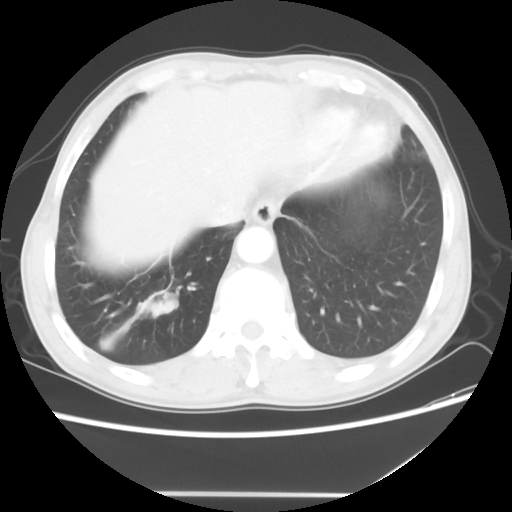
Chest CT, one axial slice; slice 9 of 56 in the series (ordered by position); lung window (W 1500 / L -600 HU); 512 × 512 image matrix, field of view 344 × 344 mm. Patient: male, 65 years. Case-level facts recorded for this patient, not image findings: clinical TNM (as recorded): T1c N3 M0; histopathological grade: G3.
Outlined on this slice (bounding box drawn by a radiologist):
- lung tumour (recorded histology: small cell carcinoma): bounding box [x1, y1, x2, y2] px = [139, 287, 182, 321]